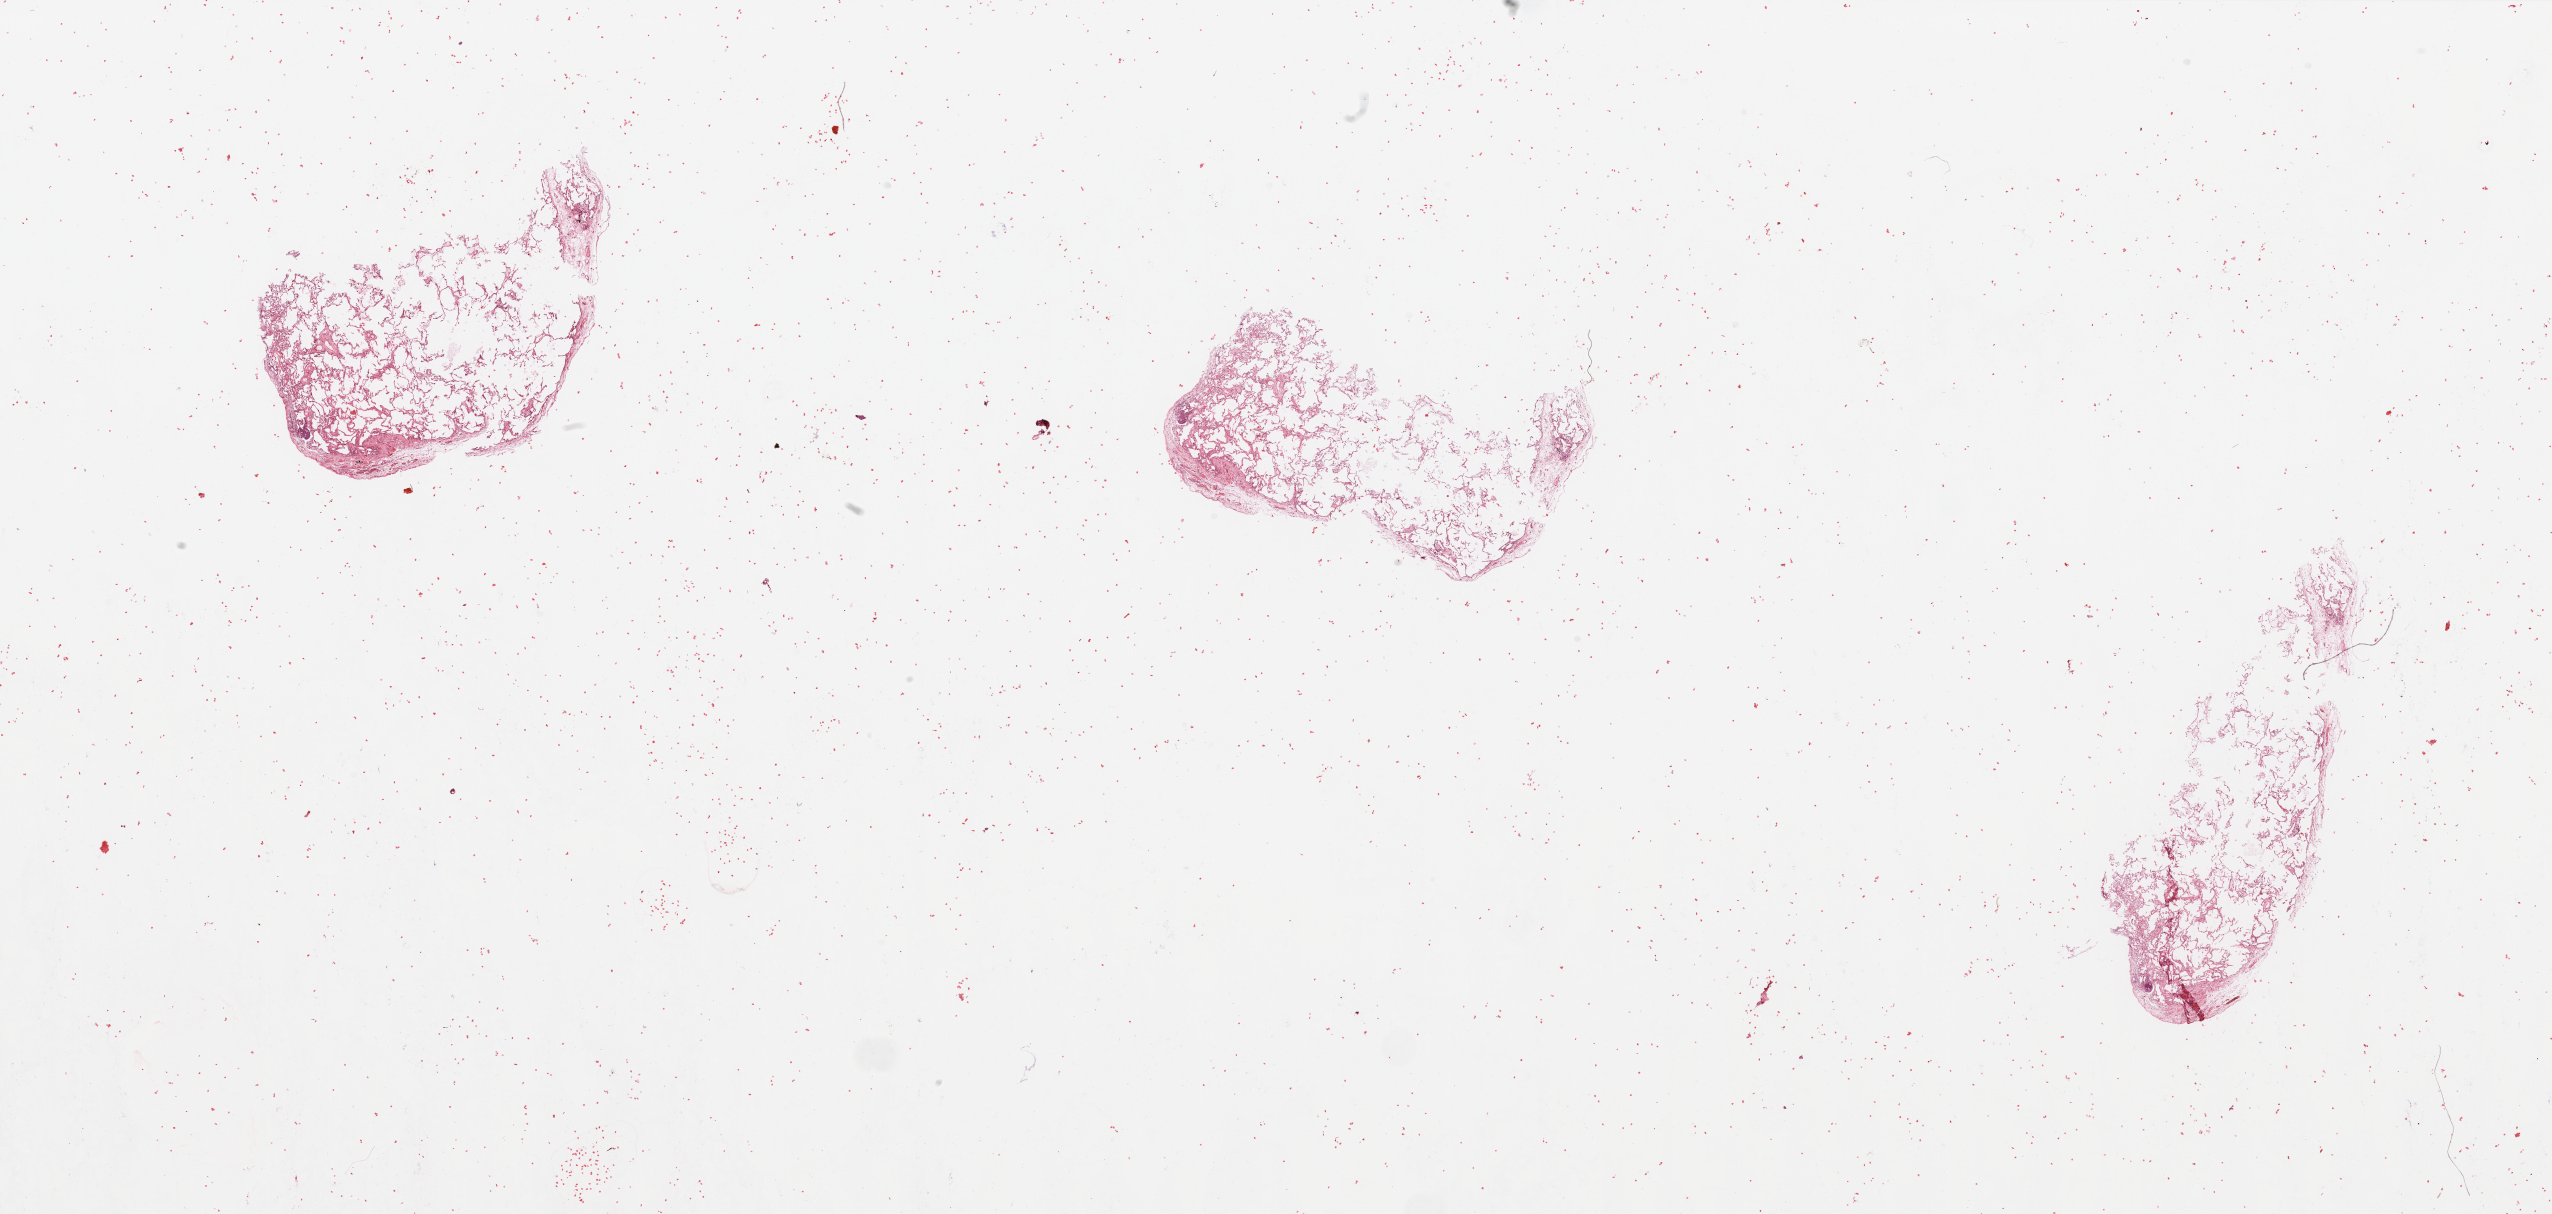
Hematoxylin and eosin (H&E) stained whole-slide image, a low-resolution overview of the entire scanned area, about 40.4 x 19.2 mm; normal (non-tumour) tissue sample, sampled site: lung. Patient: male, age 77 years.
• this section: normal (non-tumour) tissue from the same patient
• patient diagnosis: Squamous cell carcinoma, NOS